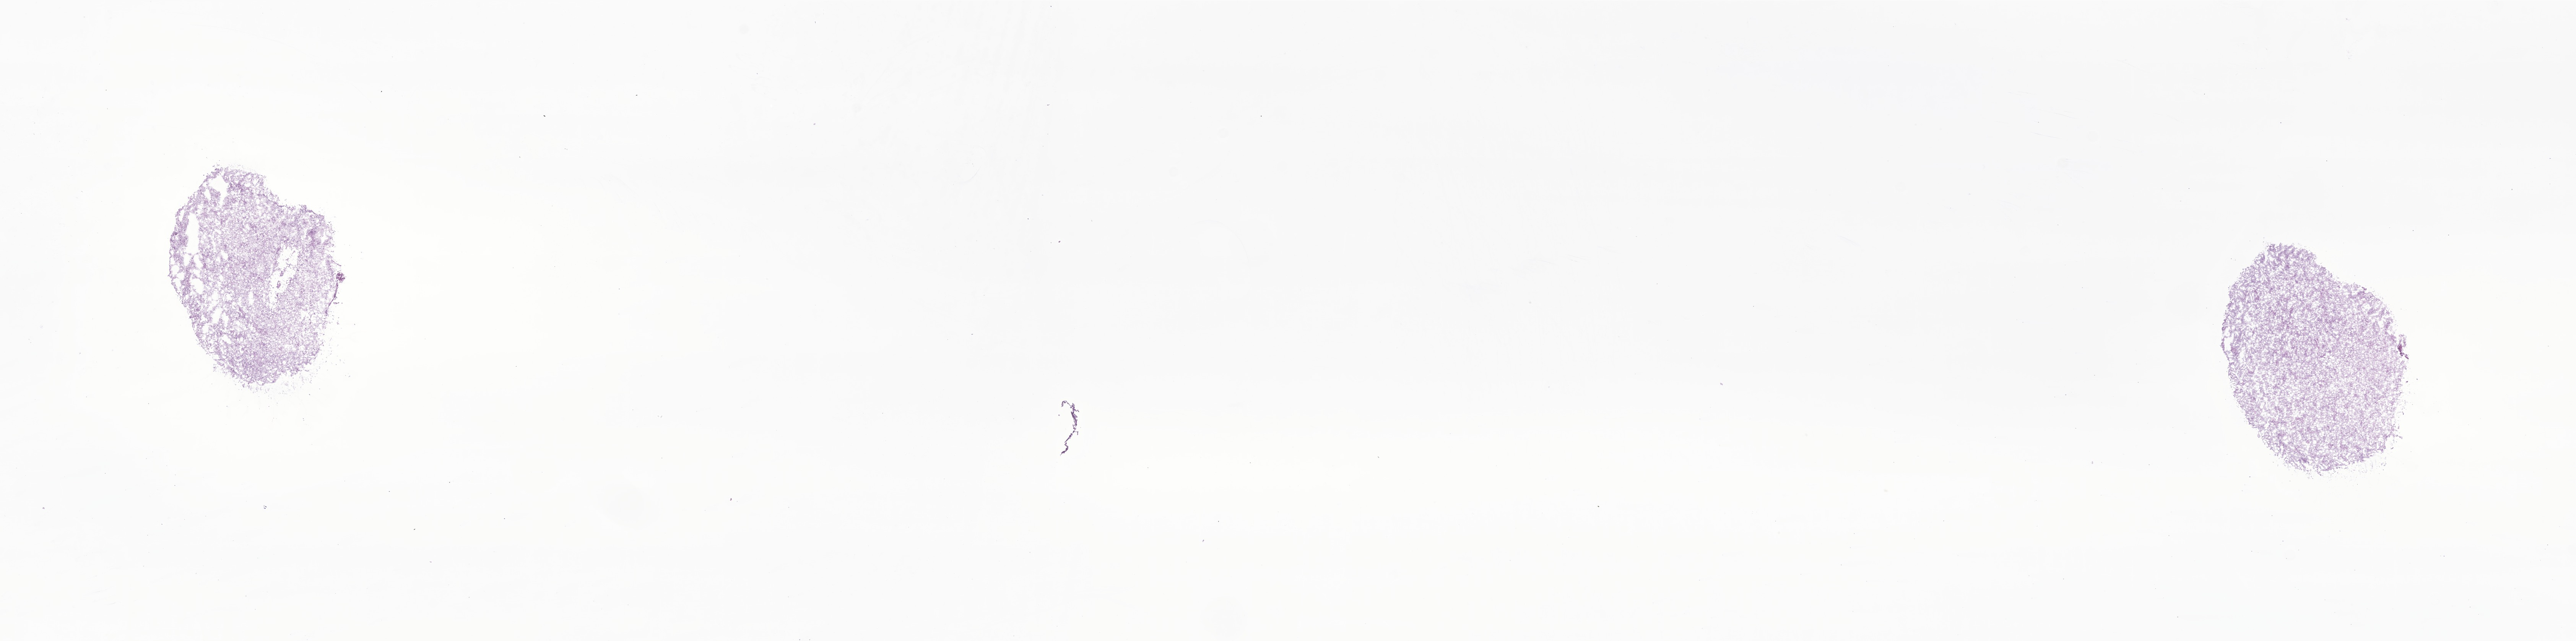
Whole-slide image, H&E stain of tumor tissue from the brain — a low-resolution overview of the entire scanned area, about 28.4 x 7.1 mm; cryosection (OCT / tissue freezing medium). Patient: male, age 128 months (10 years 8 months).
Recorded diagnosis: Glioma, malignant.